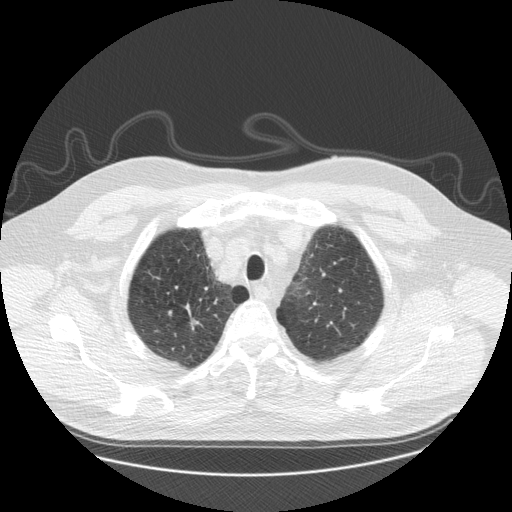
Low-dose screening chest CT, one axial slice. Position 147 of 173 along the scan axis. Reconstruction kernel STANDARD. Lung window (W 1500 / L -600 HU). 2.5 mm slice thickness. 512 × 512 image matrix.
Outlined on this slice (outlined manually by an expert reader):
- lesion 1 (tumor, upper lobe of right lung): box from (x=191, y=321) to (x=199, y=330) px